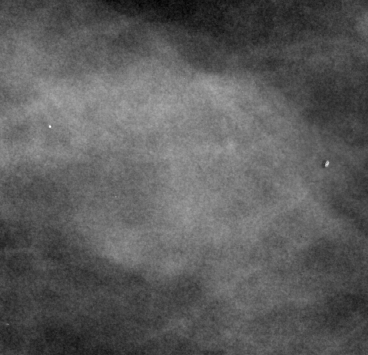
Cropped region of a digitized screen-film mammogram centred on a radiologist-marked abnormality; right breast; CC view; BI-RADS breast density category 2 (scale 1–4).
Marked abnormality: mass, shape lobulated, margins circumscribed; BI-RADS assessment category 3; subtlety rating 5 on a 1 (subtle) to 5 (obvious) scale; pathology (as recorded): benign.